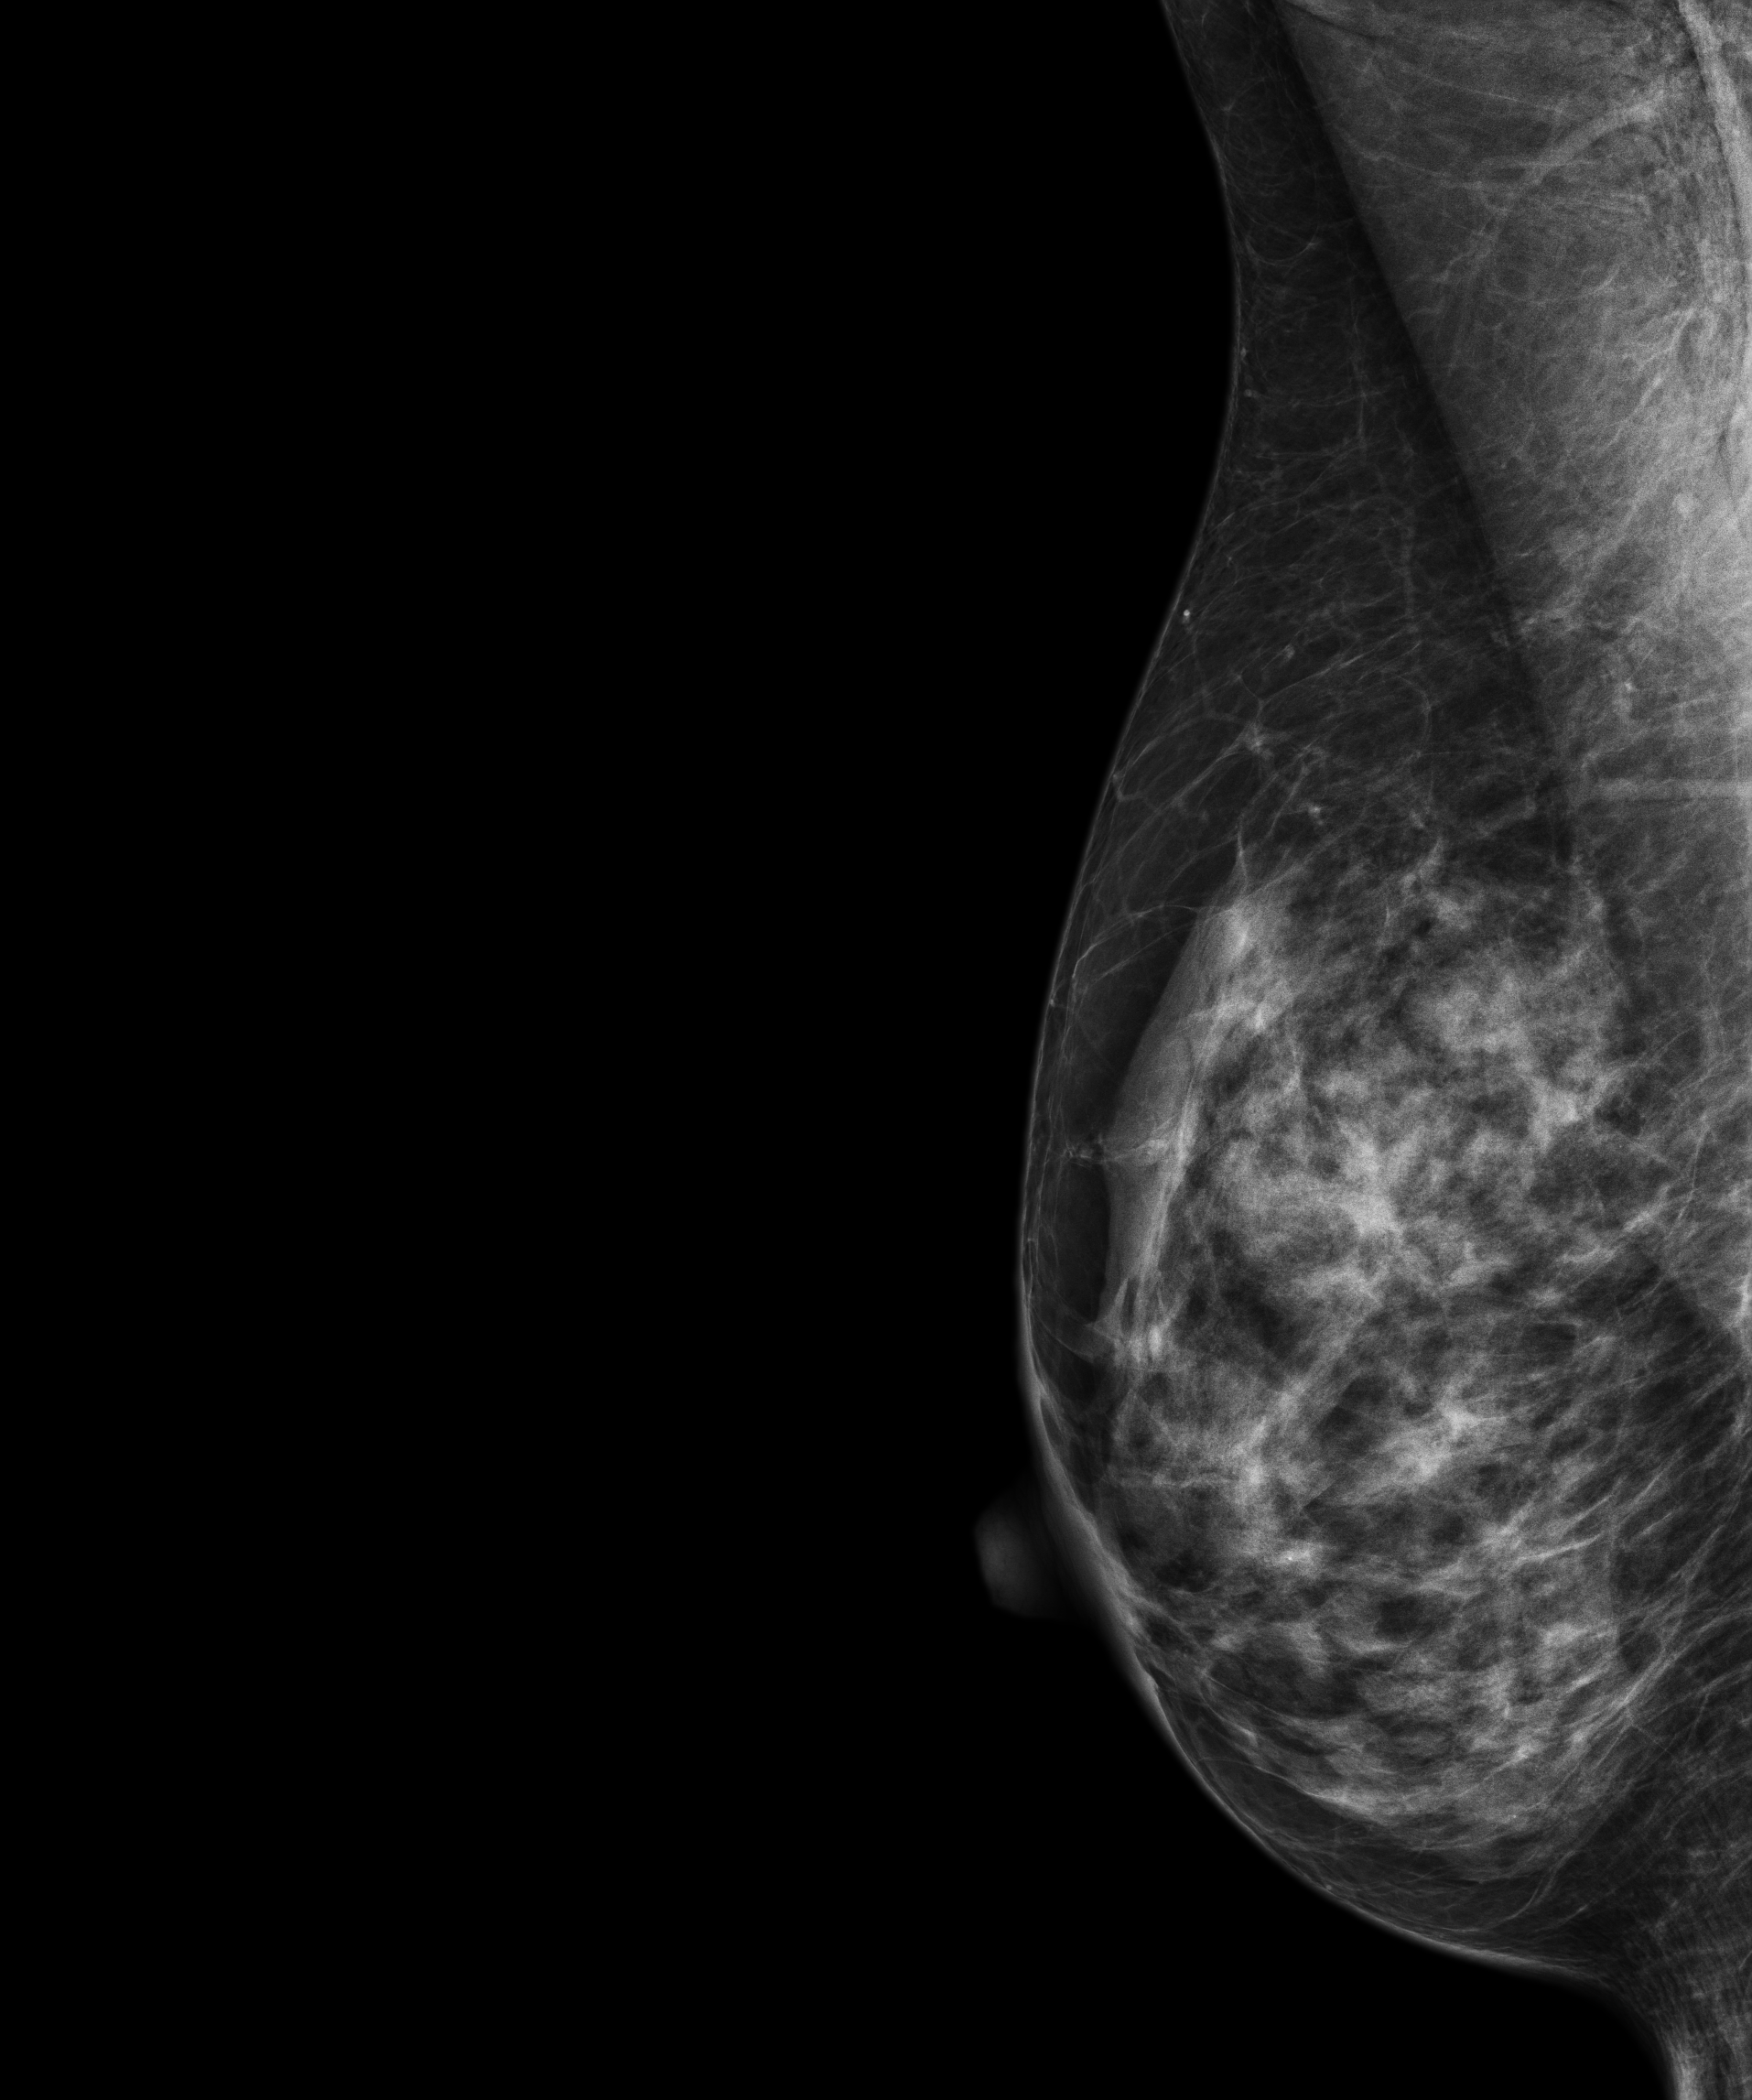
Full-field digital mammogram (FFDM), right breast, medio-lateral oblique projection, screening examination, compressed breast thickness 55 mm. Patient aged 58 years (female).
Breast density at the screening exam (both breasts): heterogeneously dense (BI-RADS density category c).